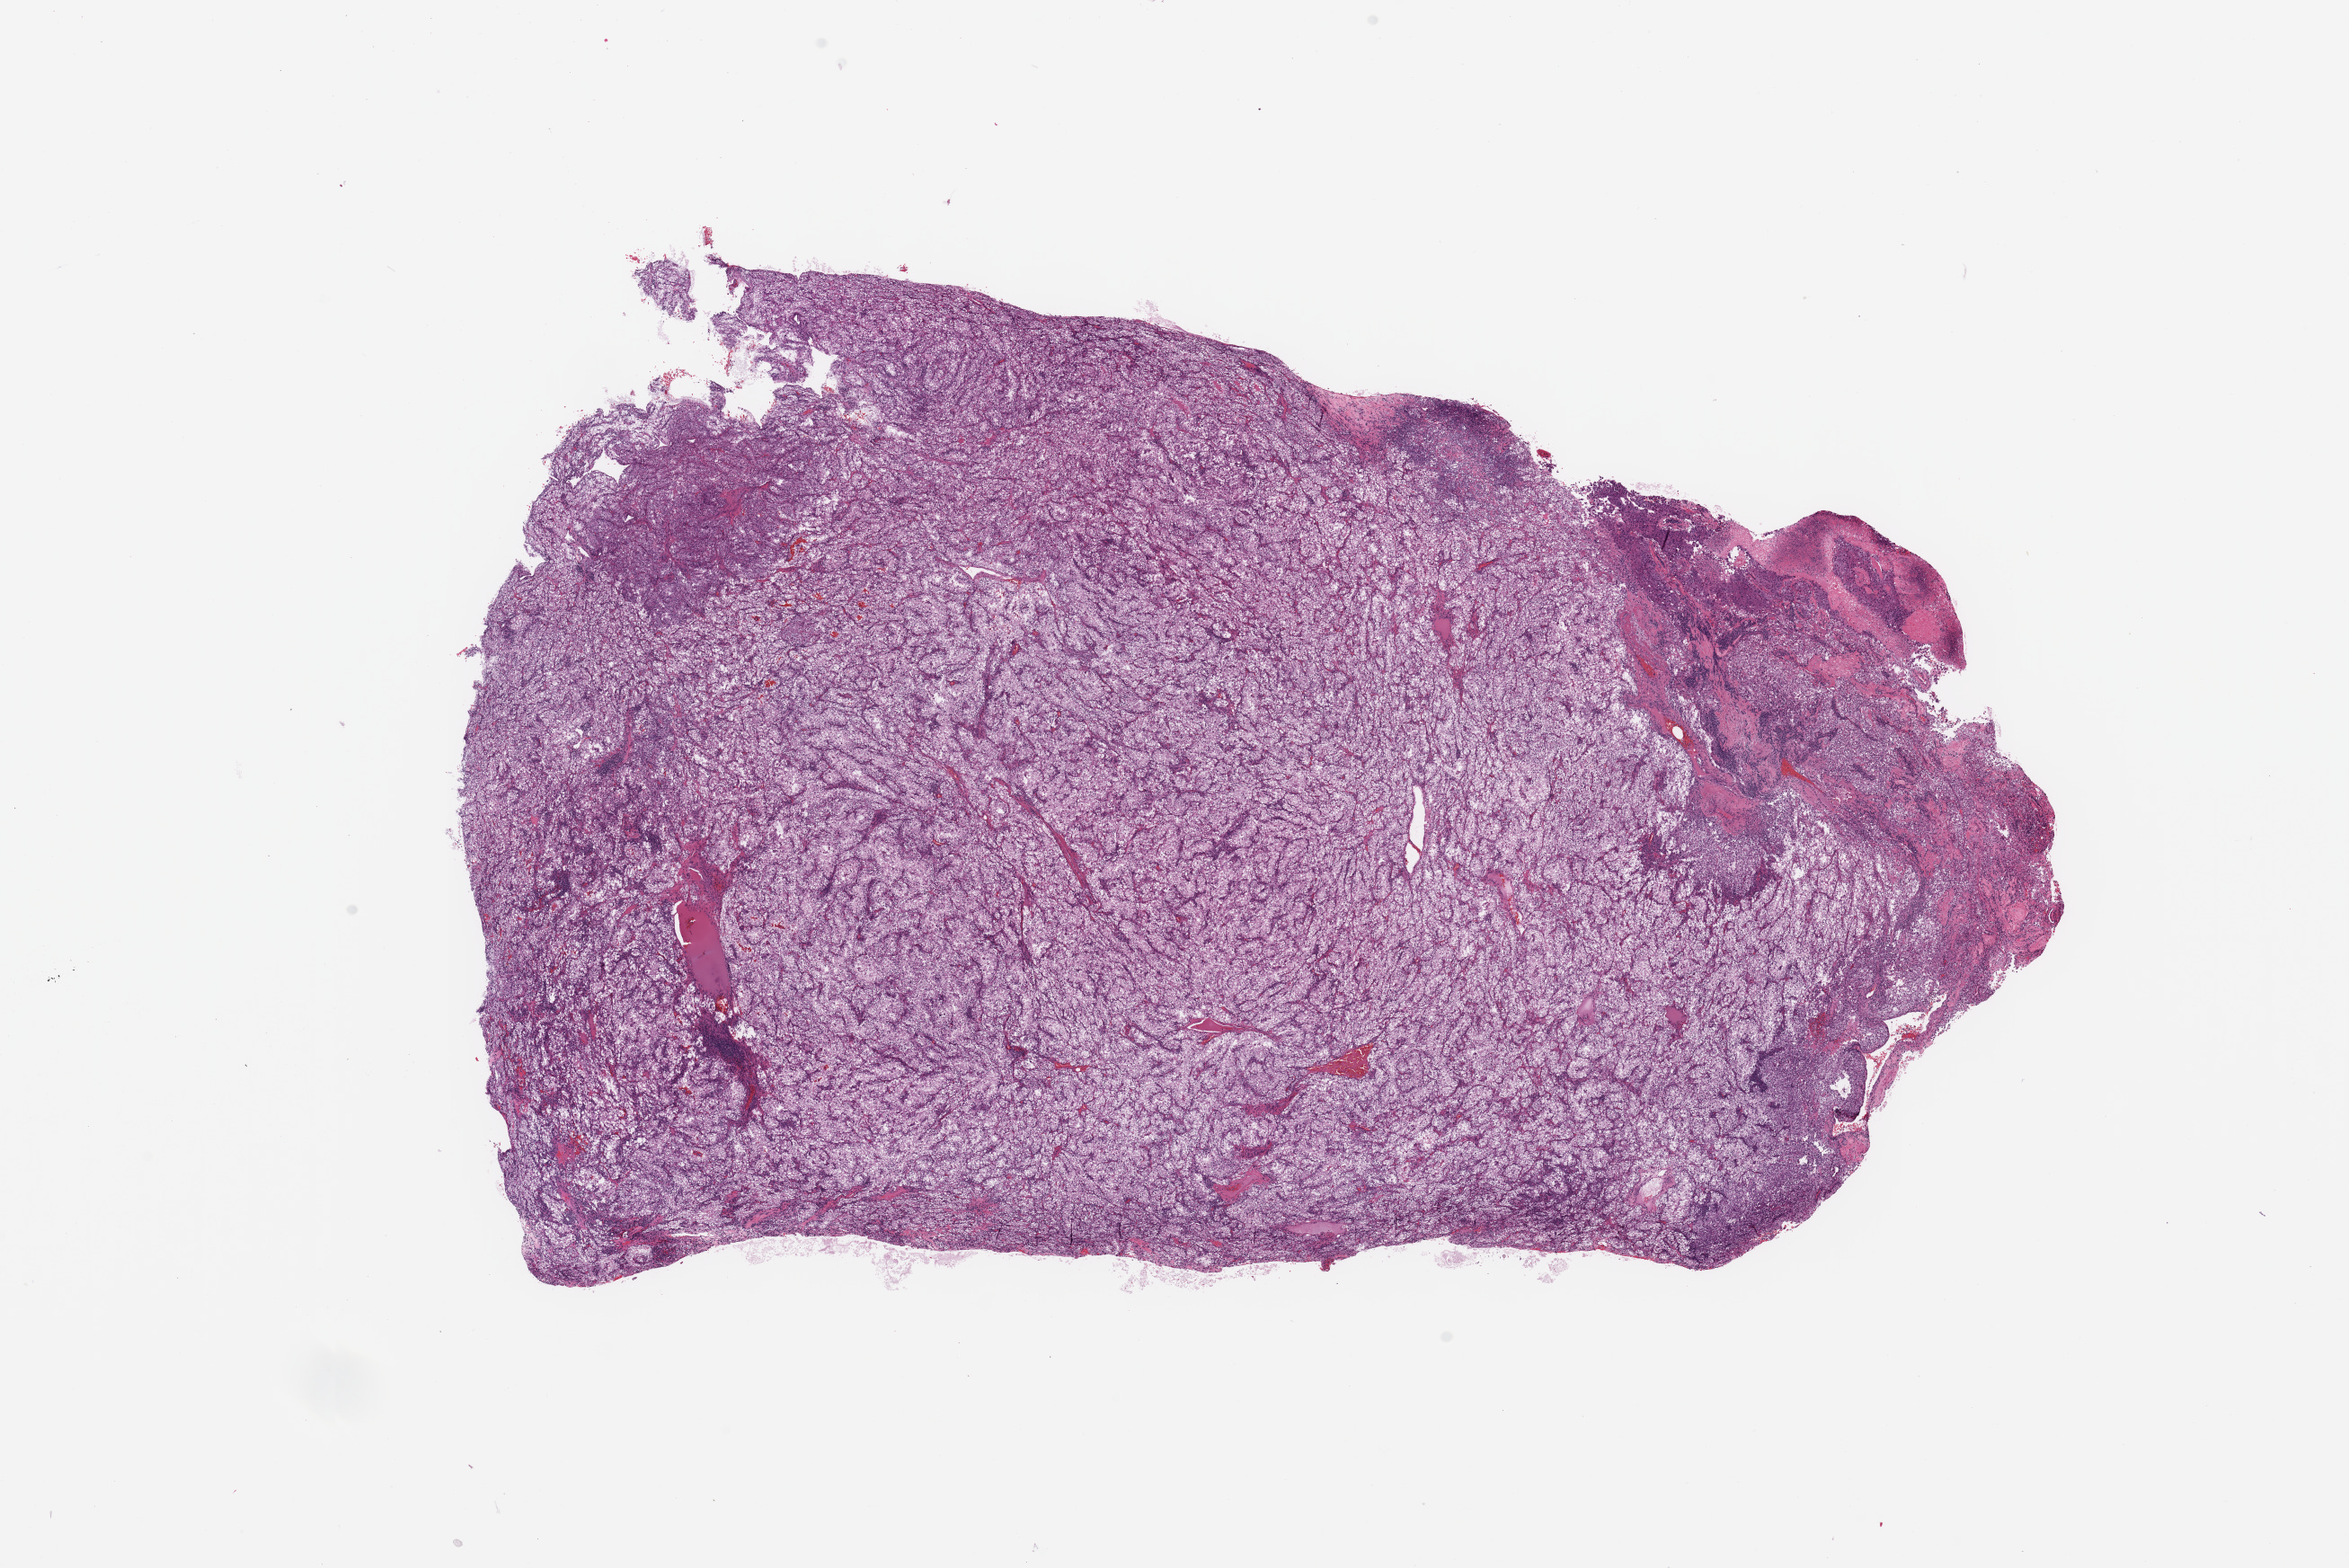
H&E-stained whole-slide image — shown as a low-resolution overview of the whole scanned area (about 20.7 x 13.8 mm, from a 20x scan); tumour tissue sample, kidney. 40-year-old male patient. Histologic grade: G3 (poorly differentiated).
* histologic diagnosis: Renal cell carcinoma, NOS
* AJCC pathologic stage: IV